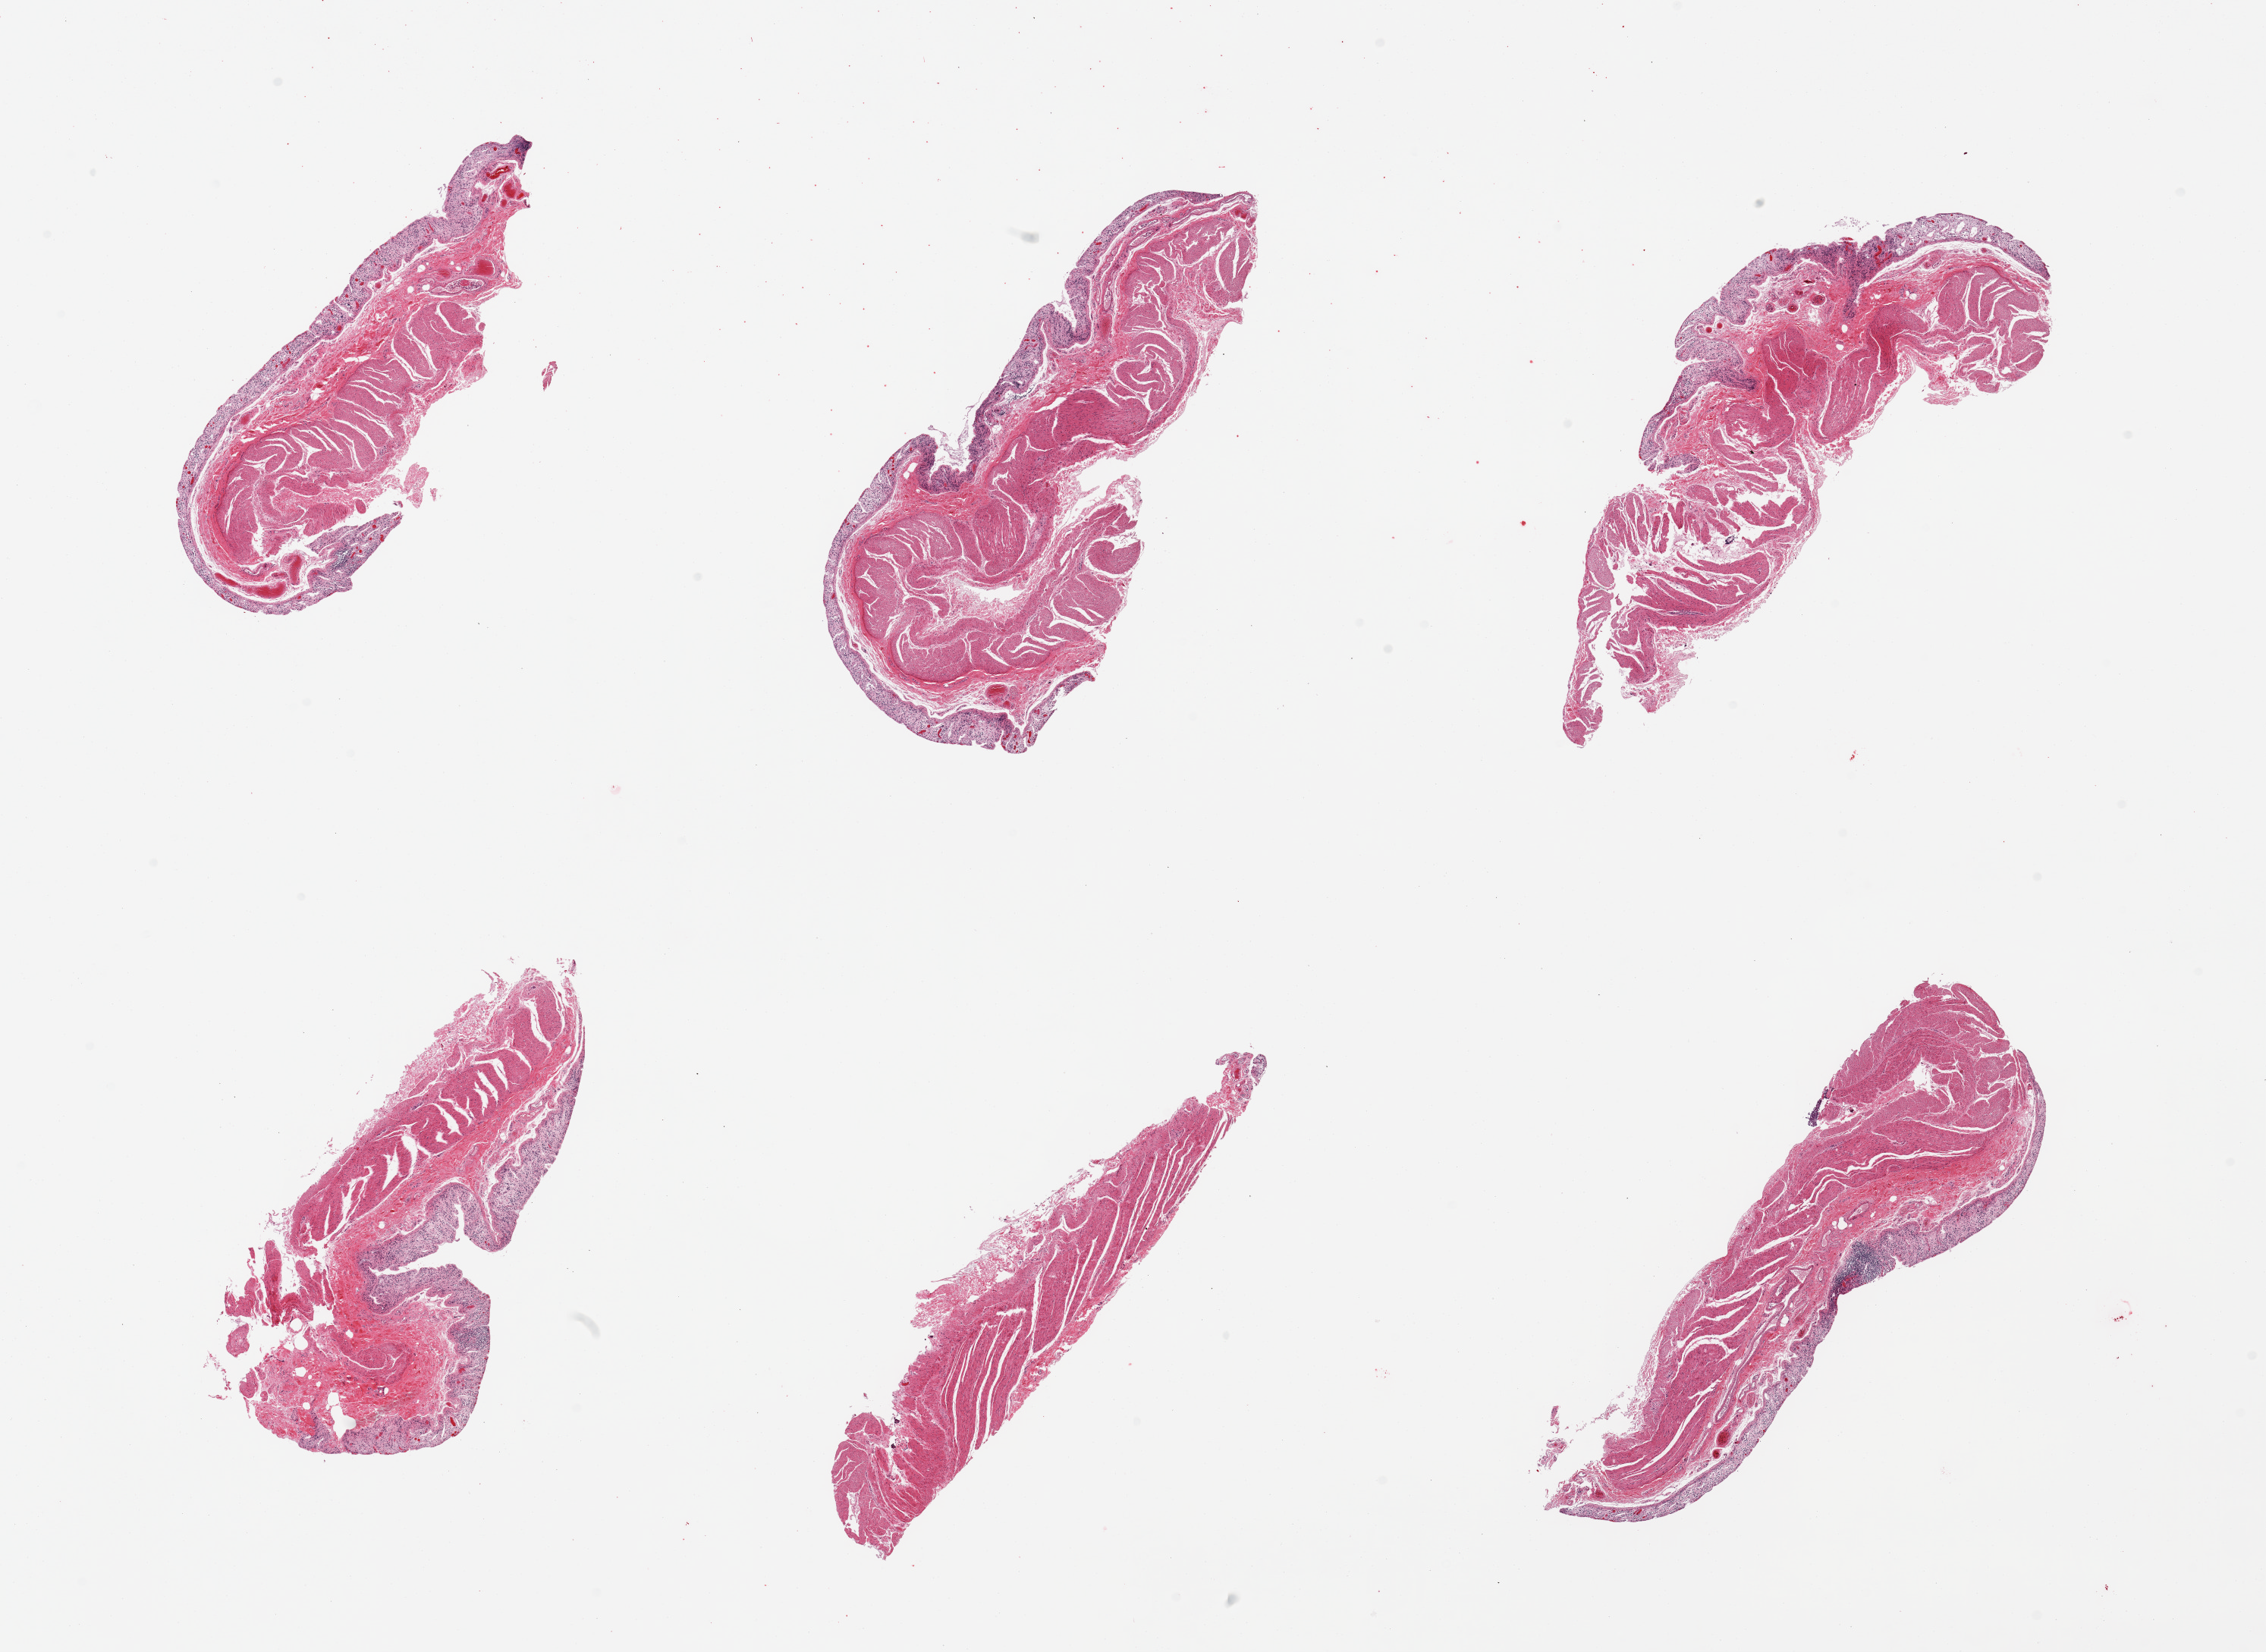
Hematoxylin and eosin (H&E) whole-slide image, brightfield, low-resolution overview of the scanned area, about 23.6 x 17.2 mm (acquisition: 20x scan); PAXgene-fixed paraffin-embedded (PFPE) section; section of transverse colon (target tissue); donor tissue sample. Donor: female.
Reviewer comment on this tissue sample: 6 pieces; moderately to severely autolyzed mucosa and better preserved muscularis; congestion.